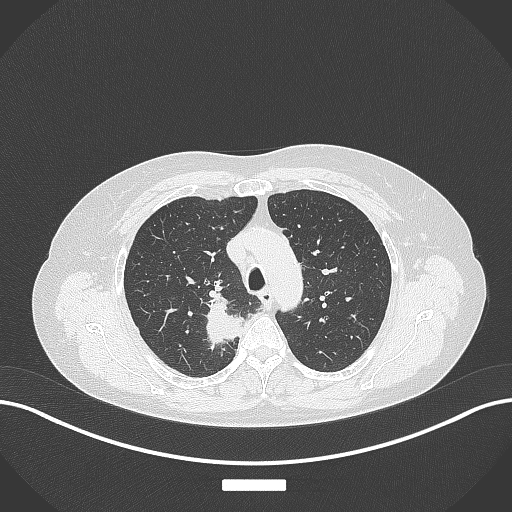
Chest CT, one axial slice; slice 287 of 357 in the series (ordered by position); reconstruction kernel B70f; 120 kVp; lung window (W 1500 / L -600 HU); 1 mm slice thickness; 512 × 512 image matrix, field of view 400 × 400 mm. Female patient, age 62 years. Case-level facts recorded for this patient, not image findings: clinical TNM (as recorded): T1c N1 M0.
Annotated regions visible in this slice (bounding box drawn by a radiologist):
- lung tumour (recorded histology: squamous cell carcinoma): box from (x=201, y=297) to (x=247, y=352) px